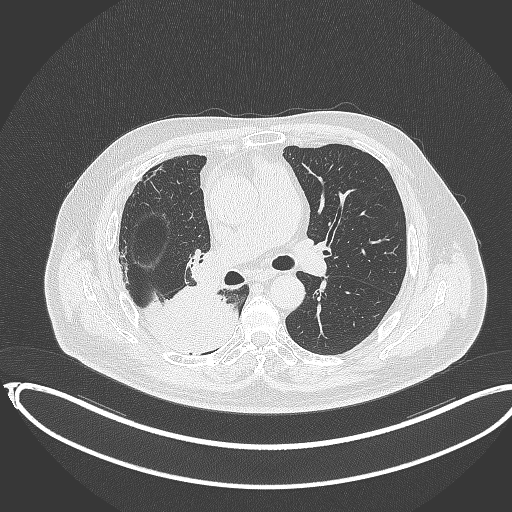
Chest CT, one axial slice; reconstruction kernel B70f; lung window (W 1500 / L -600 HU); 1 mm slice thickness; 512 × 512 image matrix. Male patient, age 68 years. From the clinical record (not read from this slice): clinical TNM (as recorded): T2a N0 M0.
Outlined on this slice (rectangle marked by the reading radiologist):
- lung tumour (recorded histology: adenocarcinoma): box from (x=144, y=287) to (x=242, y=353) px